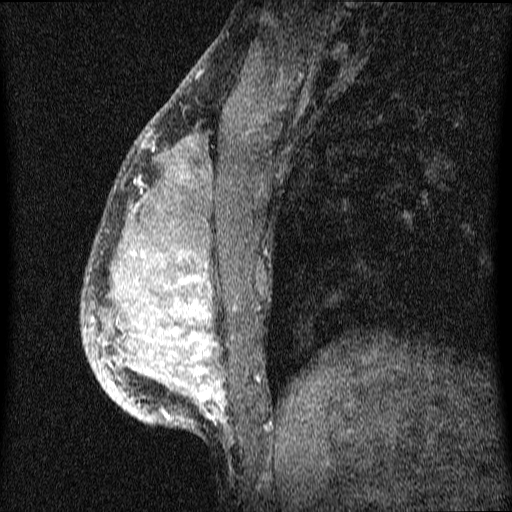
Breast MRI (dynamic contrast-enhanced), one sagittal slice; position 23 of 64 along the scan axis; dynamic contrast-enhanced series, image 2 of 4 at this slice position (ordered by acquisition); 1.5 T; TE 4.2 ms, TR 9.1 ms; 512 × 512 image matrix. Patient: female, 33 years.
Structures marked on this image (semi-automatic segmentation, software-assisted and operator-edited):
- analysis volume of interest (the breast-tissue region the enhancement analysis was run in; not a lesion): bounding box (x1, y1, x2, y2) in pixels: (82, 151, 334, 450)
- tumour enhancement mask (voxels above the 70 % enhancement threshold inside the analysis volume of interest): (93, 181, 226, 422)